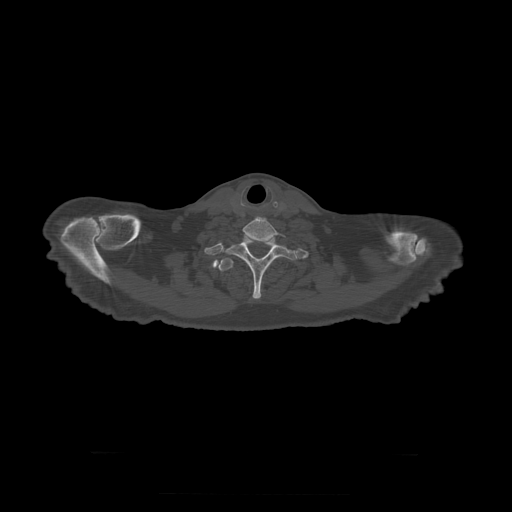
CT including the spine, one axial slice; slice 289 of 397 in the series (ordered by position); 120 kVp; bone window (W 1800 / L 400 HU); 1.25 mm slice thickness; 512 × 512 image matrix, field of view 510 × 510 mm. Patient age 73 years. From the clinical record (not read from this slice): primary cancer: prostate.
Annotated regions visible in this slice (semi-automatically segmented with operator editing):
- T1 vertebra: bounding box <227,234,297,299> (left, top, right, bottom; pixels)
- T2 vertebra: <219,258,234,272>